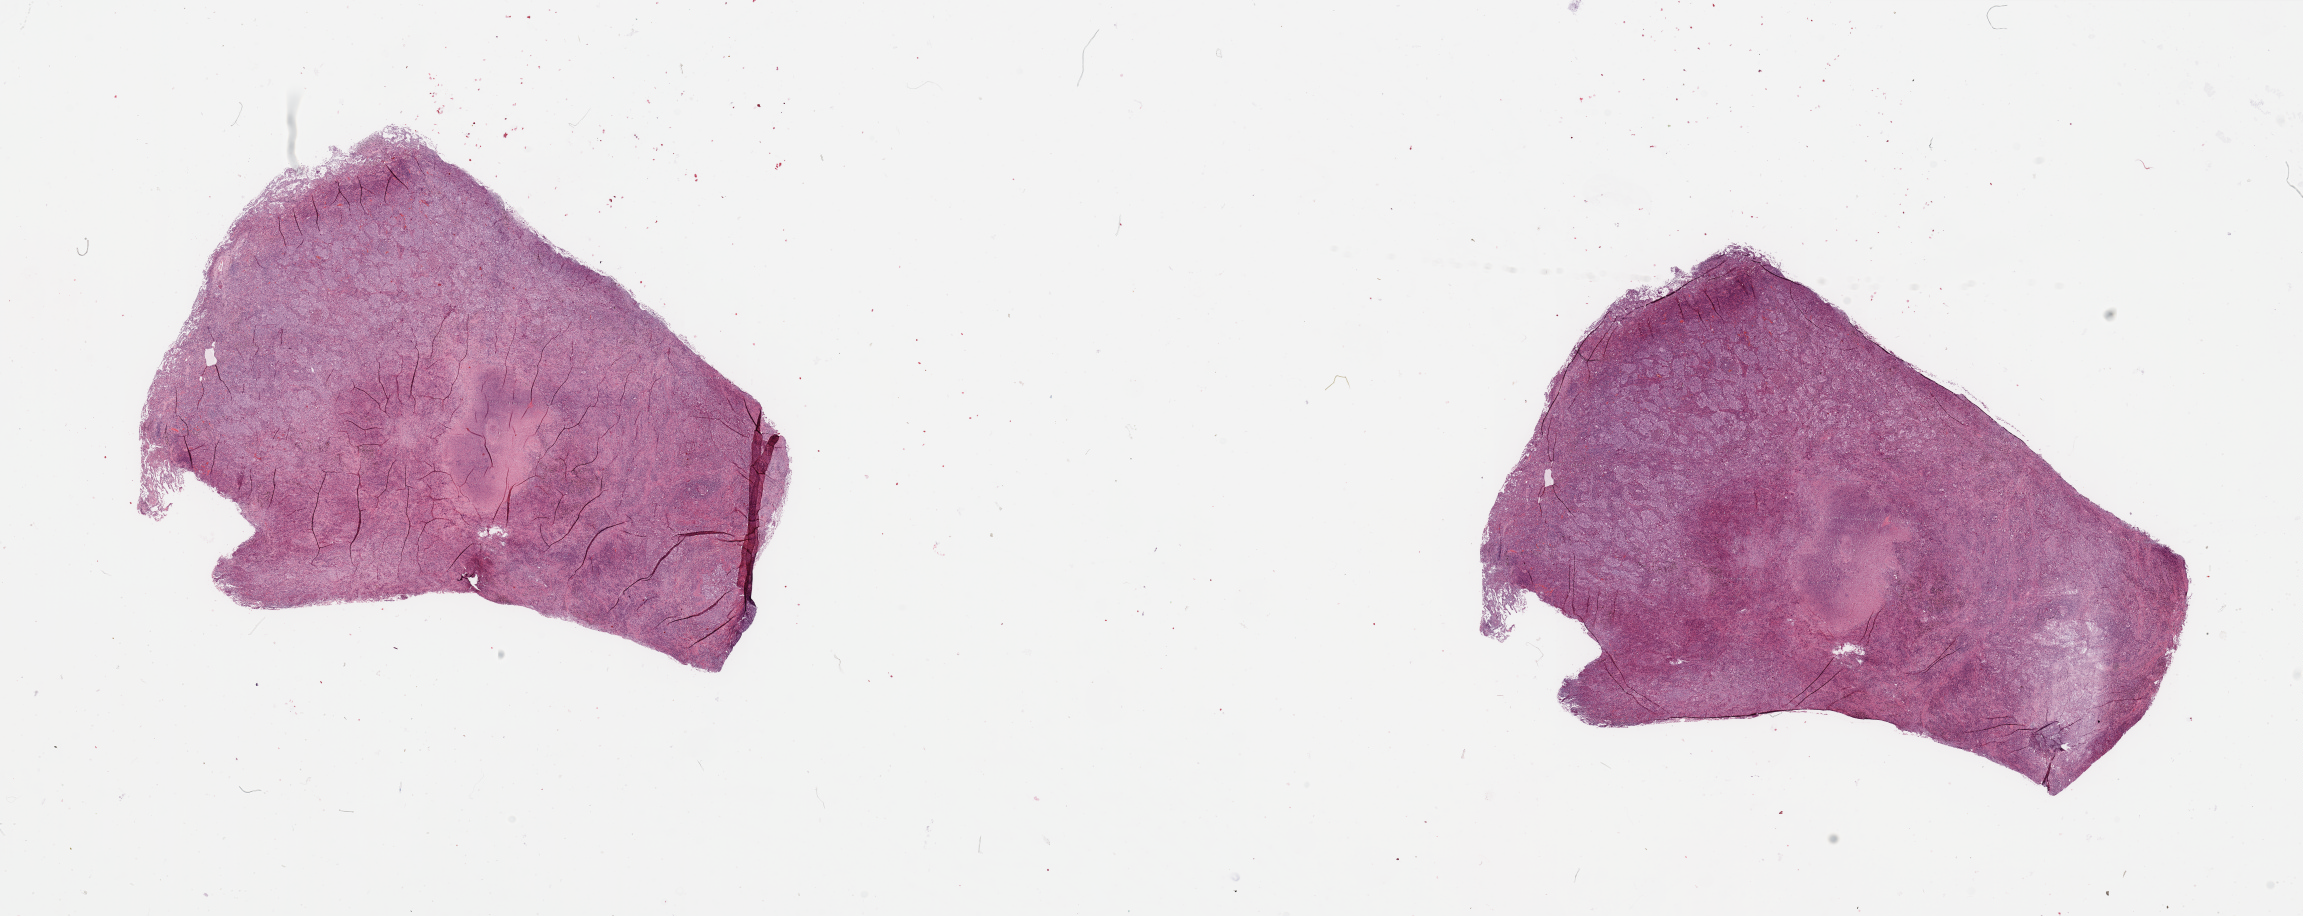
Whole-slide histology image, Hematoxylin and eosin (H&E) stained, a low-resolution overview of the entire scanned area, about 36.4 x 14.5 mm (acquisition: 20x scan); tumour tissue sample, lung. Male, 65 y/o. Histologic grade: G3 (poorly differentiated).
Diagnosis: Adenocarcinoma, NOS. AJCC pathologic stage: IIIA.